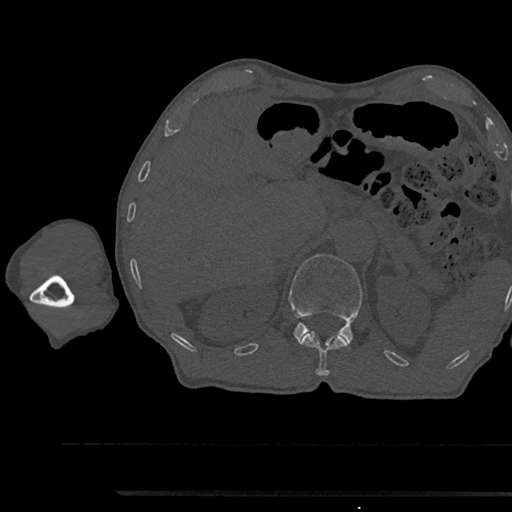
CT including the spine, one axial slice; position 675 of 797 along the scan axis; reconstruction kernel Br40s/3; 120 kVp; bone window (W 1800 / L 400 HU); 0.5 mm slice thickness; 512 × 512 image matrix, field of view 367 × 367 mm. Patient: male, 79 years. Case-level facts recorded for this patient, not image findings: primary cancer: prostate.
Annotated regions visible in this slice (semi-automatically segmented with operator editing):
- L1 vertebra: bounding box <289,254,362,342> (left, top, right, bottom; pixels)
- T12 vertebra: <248,331,350,376>